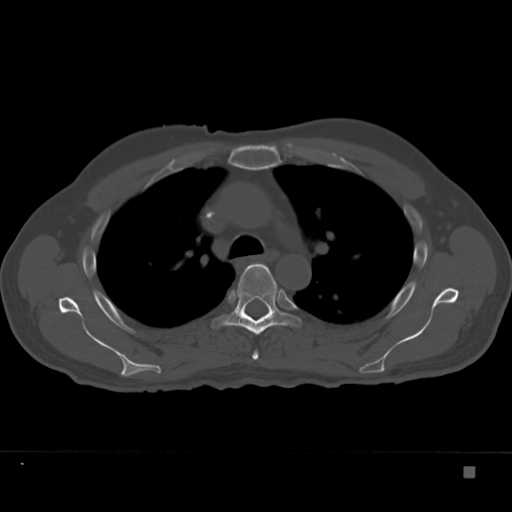
CT including the spine, one axial slice; position 259 of 332 along the scan axis; reconstruction kernel Br40s; 120 kVp; bone window (W 1800 / L 400 HU); 1.5 mm slice thickness; 512 × 512 image matrix, field of view 389 × 389 mm. Patient: male, 72 years. Case-level facts recorded for this patient, not image findings: primary cancer: skeletal.
Structures marked on this image (semi-automatically segmented with operator editing):
- T4 vertebra: box from (x=252, y=292) to (x=279, y=360) px
- T5 vertebra: (x=212, y=263)–(x=303, y=335)